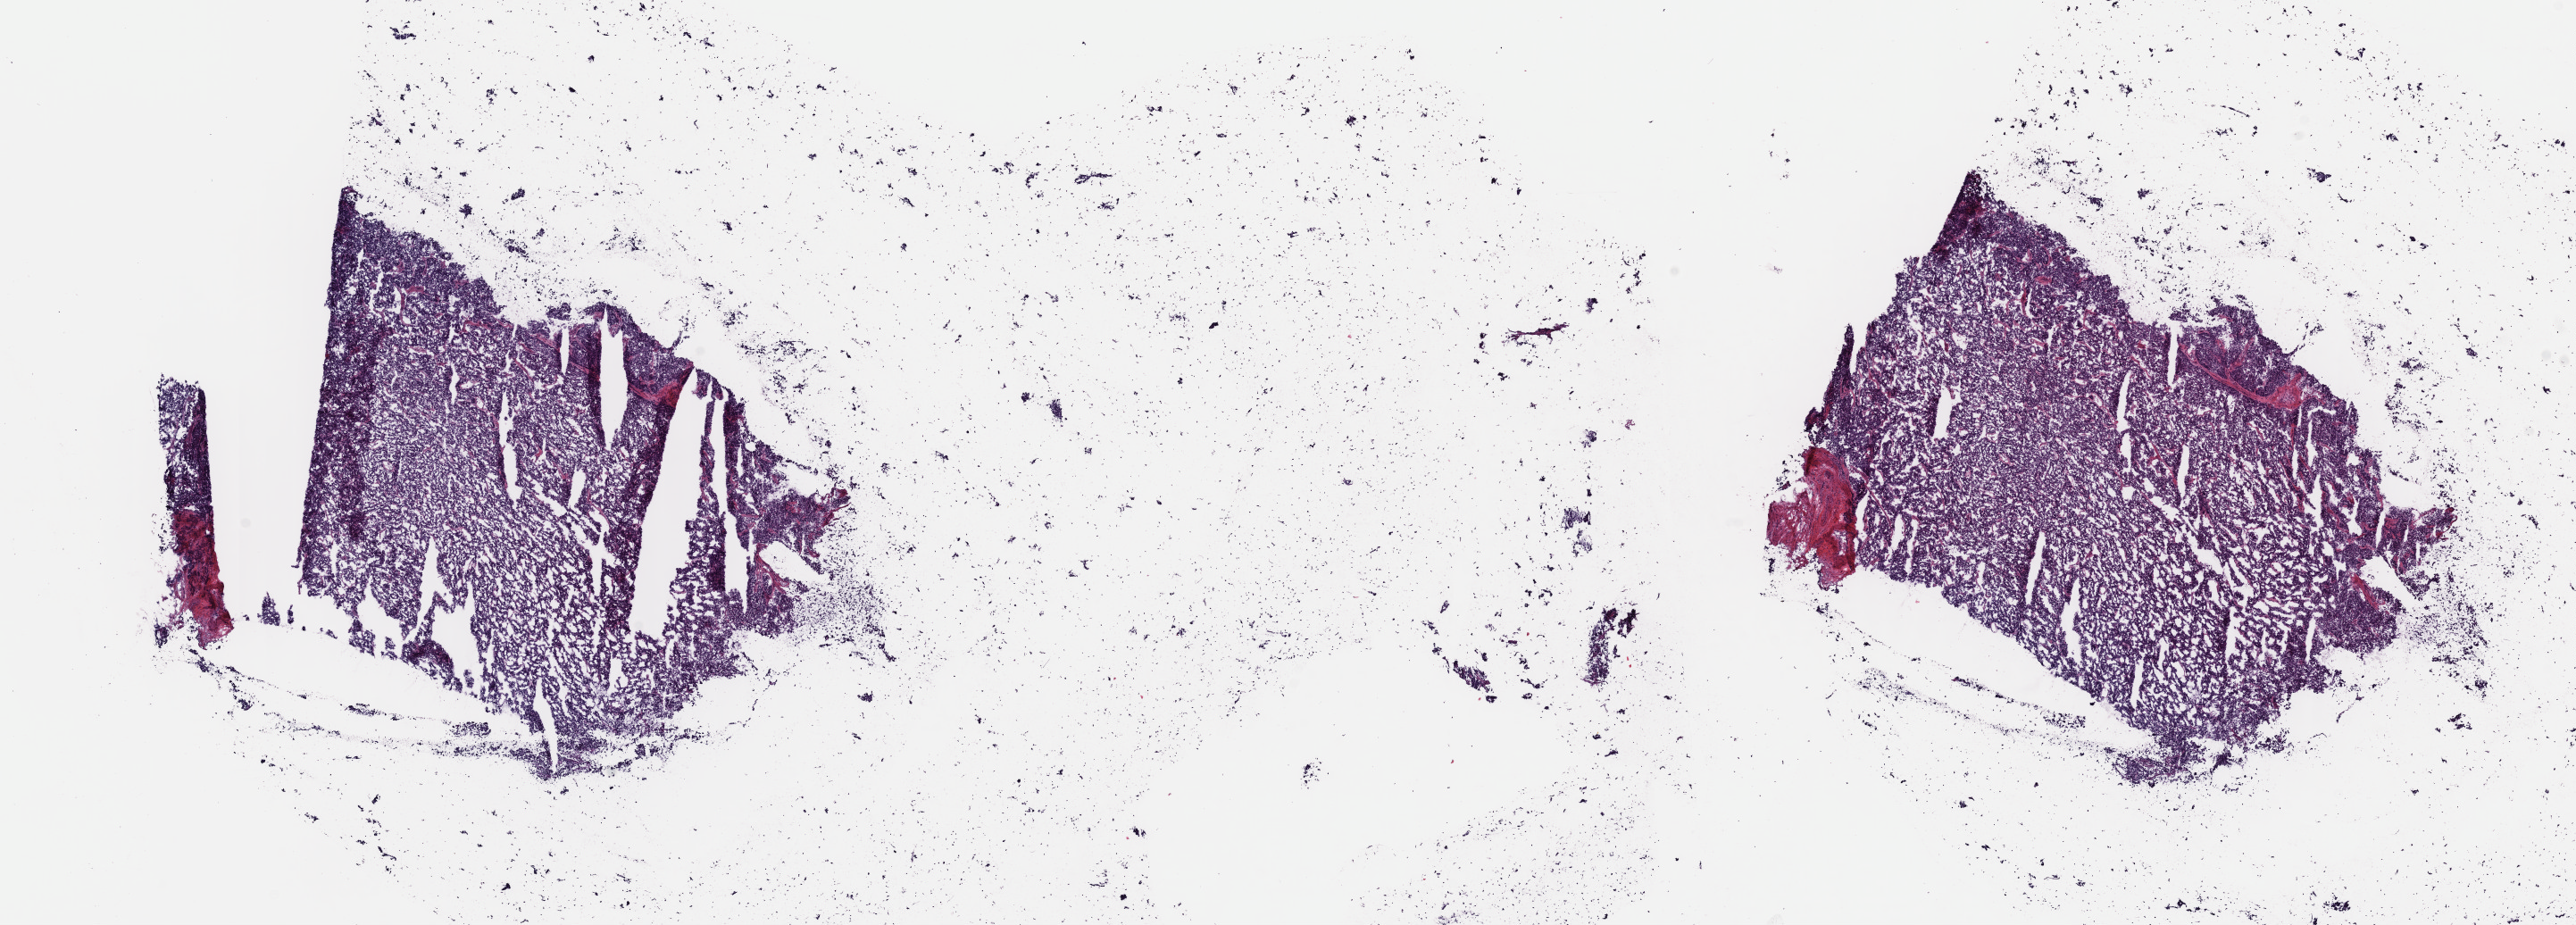
Digitized Hematoxylin and eosin (H&E) stained tissue section (whole slide), low-resolution overview of the scanned area, about 22.8 x 8.2 mm (from a 40x scan); frozen section from the top of the tissue portion; uterus, primary tumour sample. Female, age 68 years at initial diagnosis. Histologic grade: G3 (poorly differentiated). Slide review estimates, as recorded: tumour cells 80%, tumour nuclei 80%, normal cells 0%, stromal cells 10%, necrosis 10%. Inflammatory infiltration, as recorded: lymphocyte infiltration 40%, monocyte infiltration 20%, neutrophil infiltration 20%.
- diagnosis: Endometrioid adenocarcinoma, NOS (endometrium)
- FIGO stage: IIIA